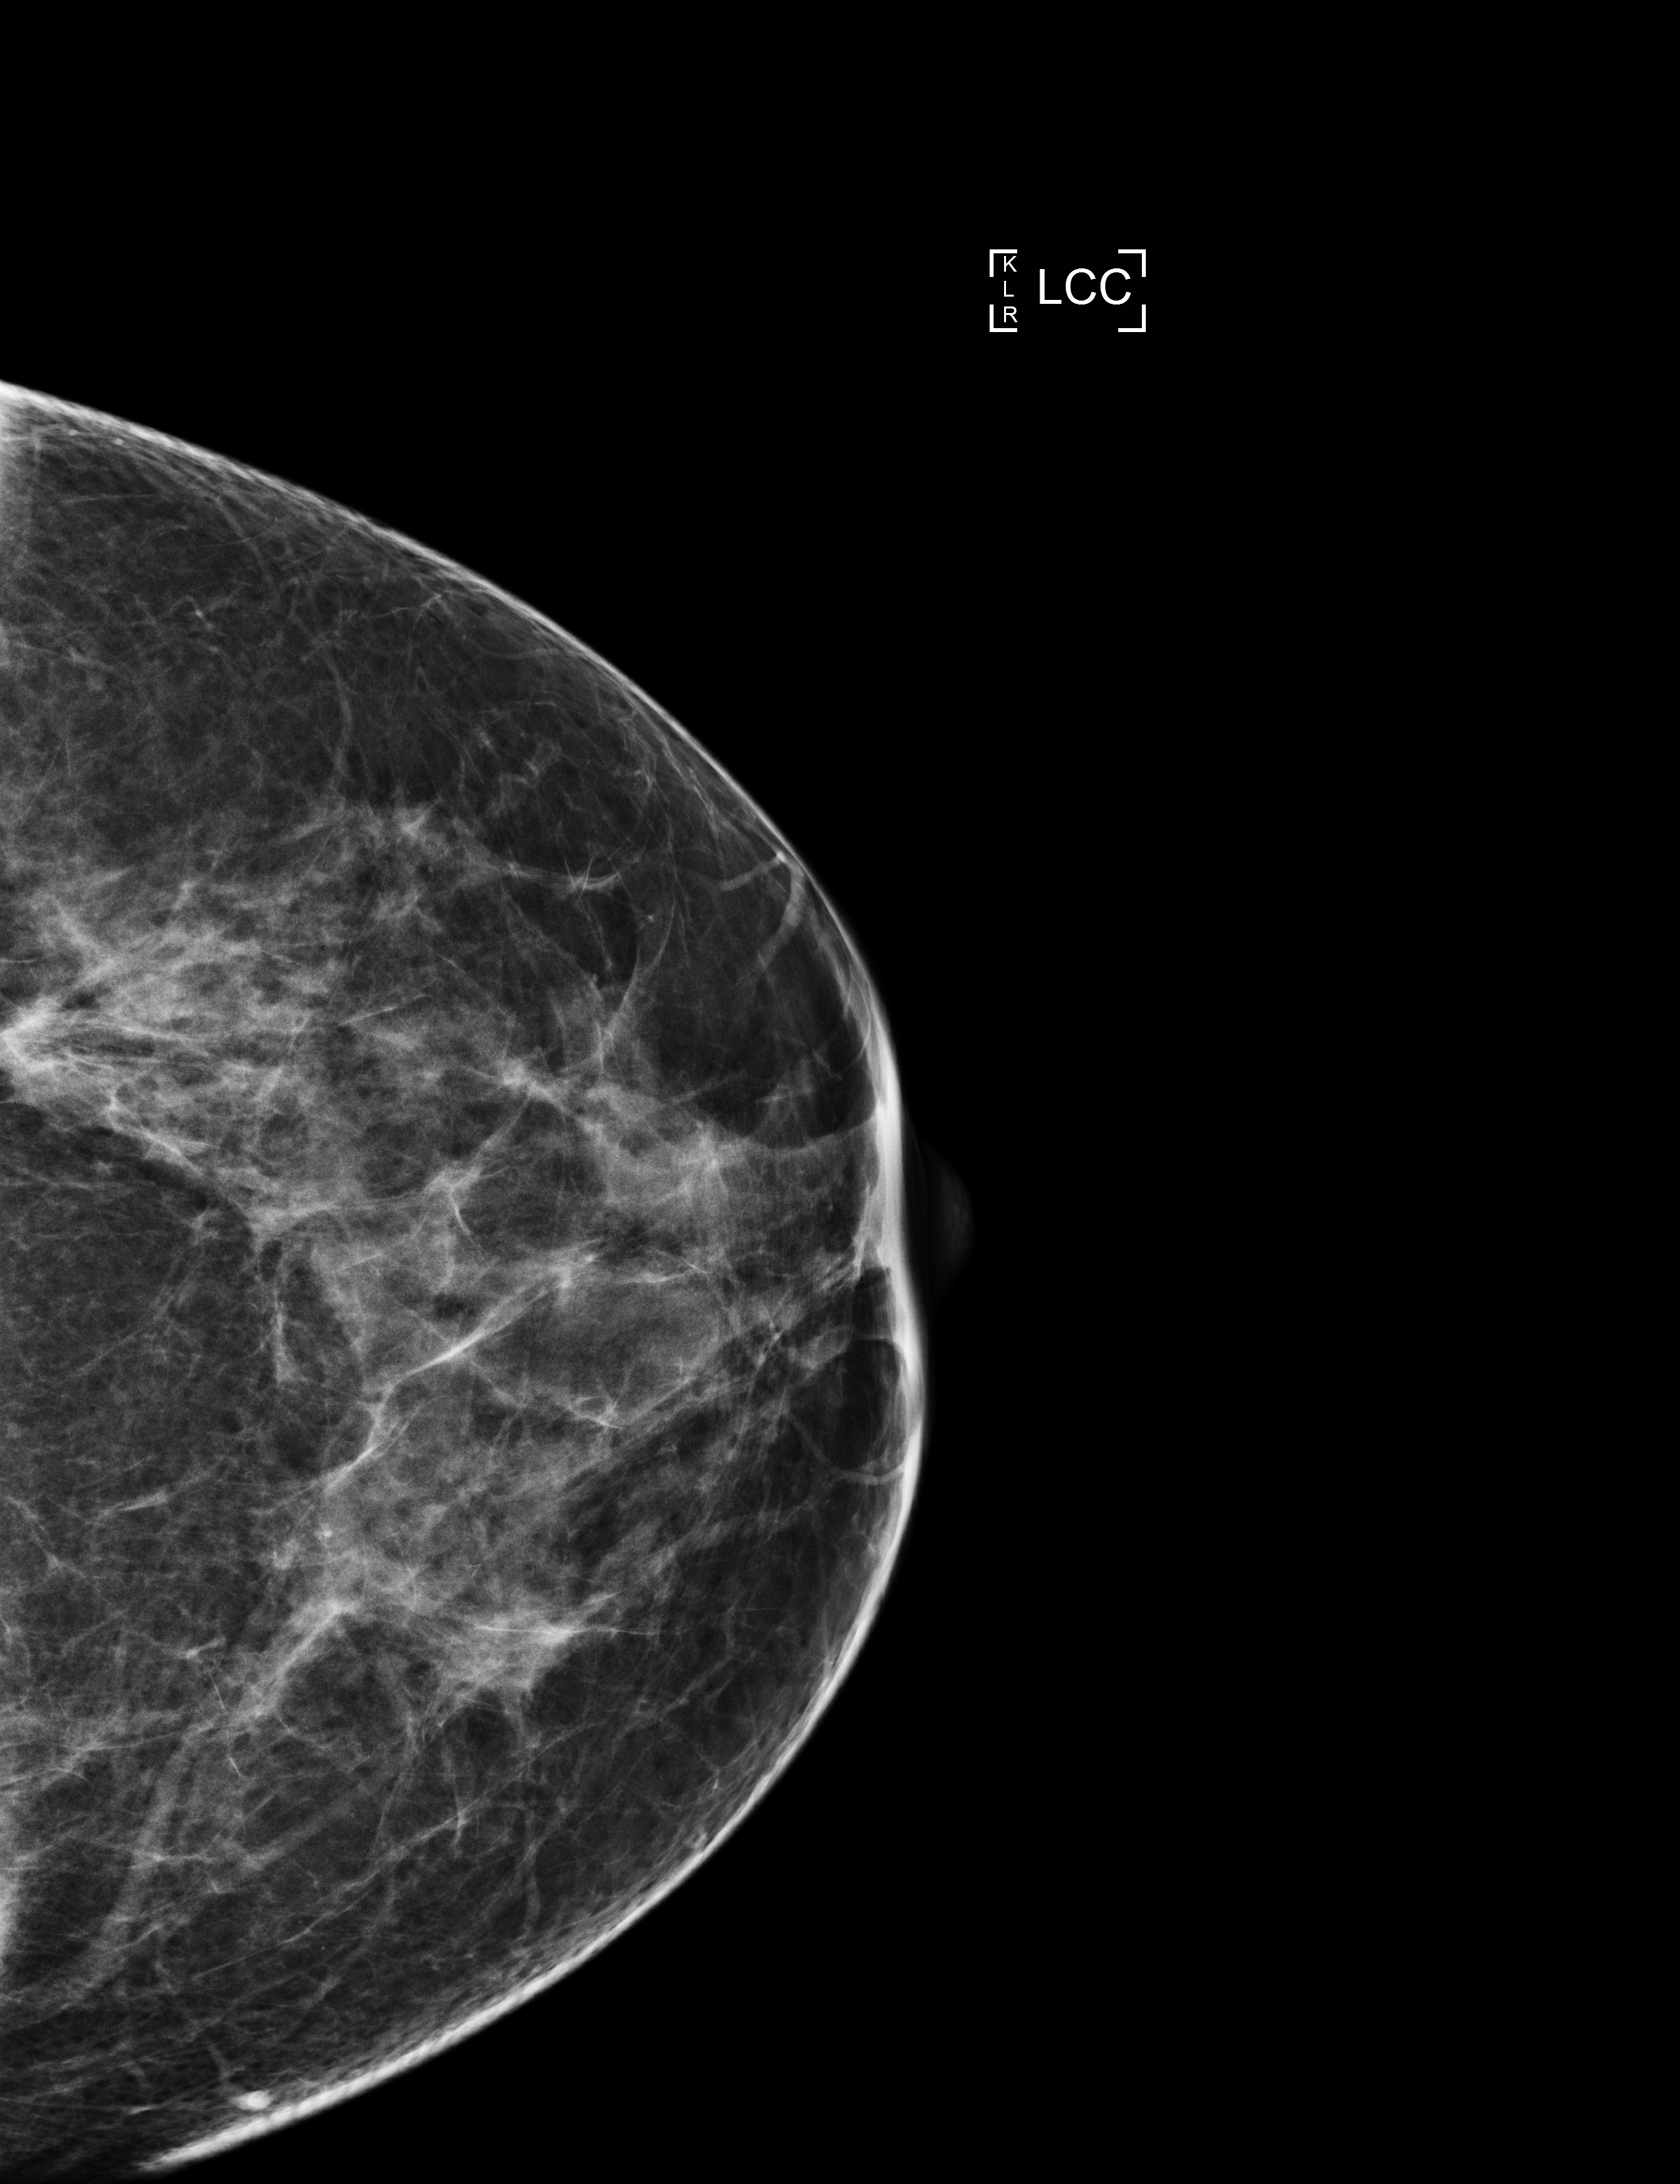
Digital mammogram (FFDM), left breast, CC view, annual screening mammography examination. Female patient, age 47 years.
- BI-RADS breast density category at the screening exam (both breasts, scale 1–4): 2
- final BI-RADS category for the screening round (tomosynthesis exam, both breasts): category 1
- recall: no recall after this screen